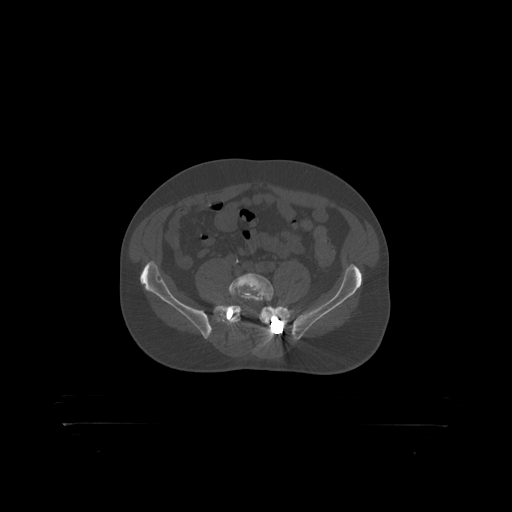
CT including the spine, one axial slice; slice 195 of 399 in the series (ordered by position); reconstruction kernel STANDARD; 120 kVp; bone window (W 1800 / L 400 HU); 1.25 mm slice thickness; 512 × 512 image matrix, field of view 650 × 650 mm. Male patient, age 46 years. Case-level facts recorded for this patient, not image findings: primary cancer: skin.
Structures marked on this image (semi-automatic segmentation, software-assisted and operator-edited):
- L5 vertebra: box from (x=230, y=273) to (x=274, y=301) px